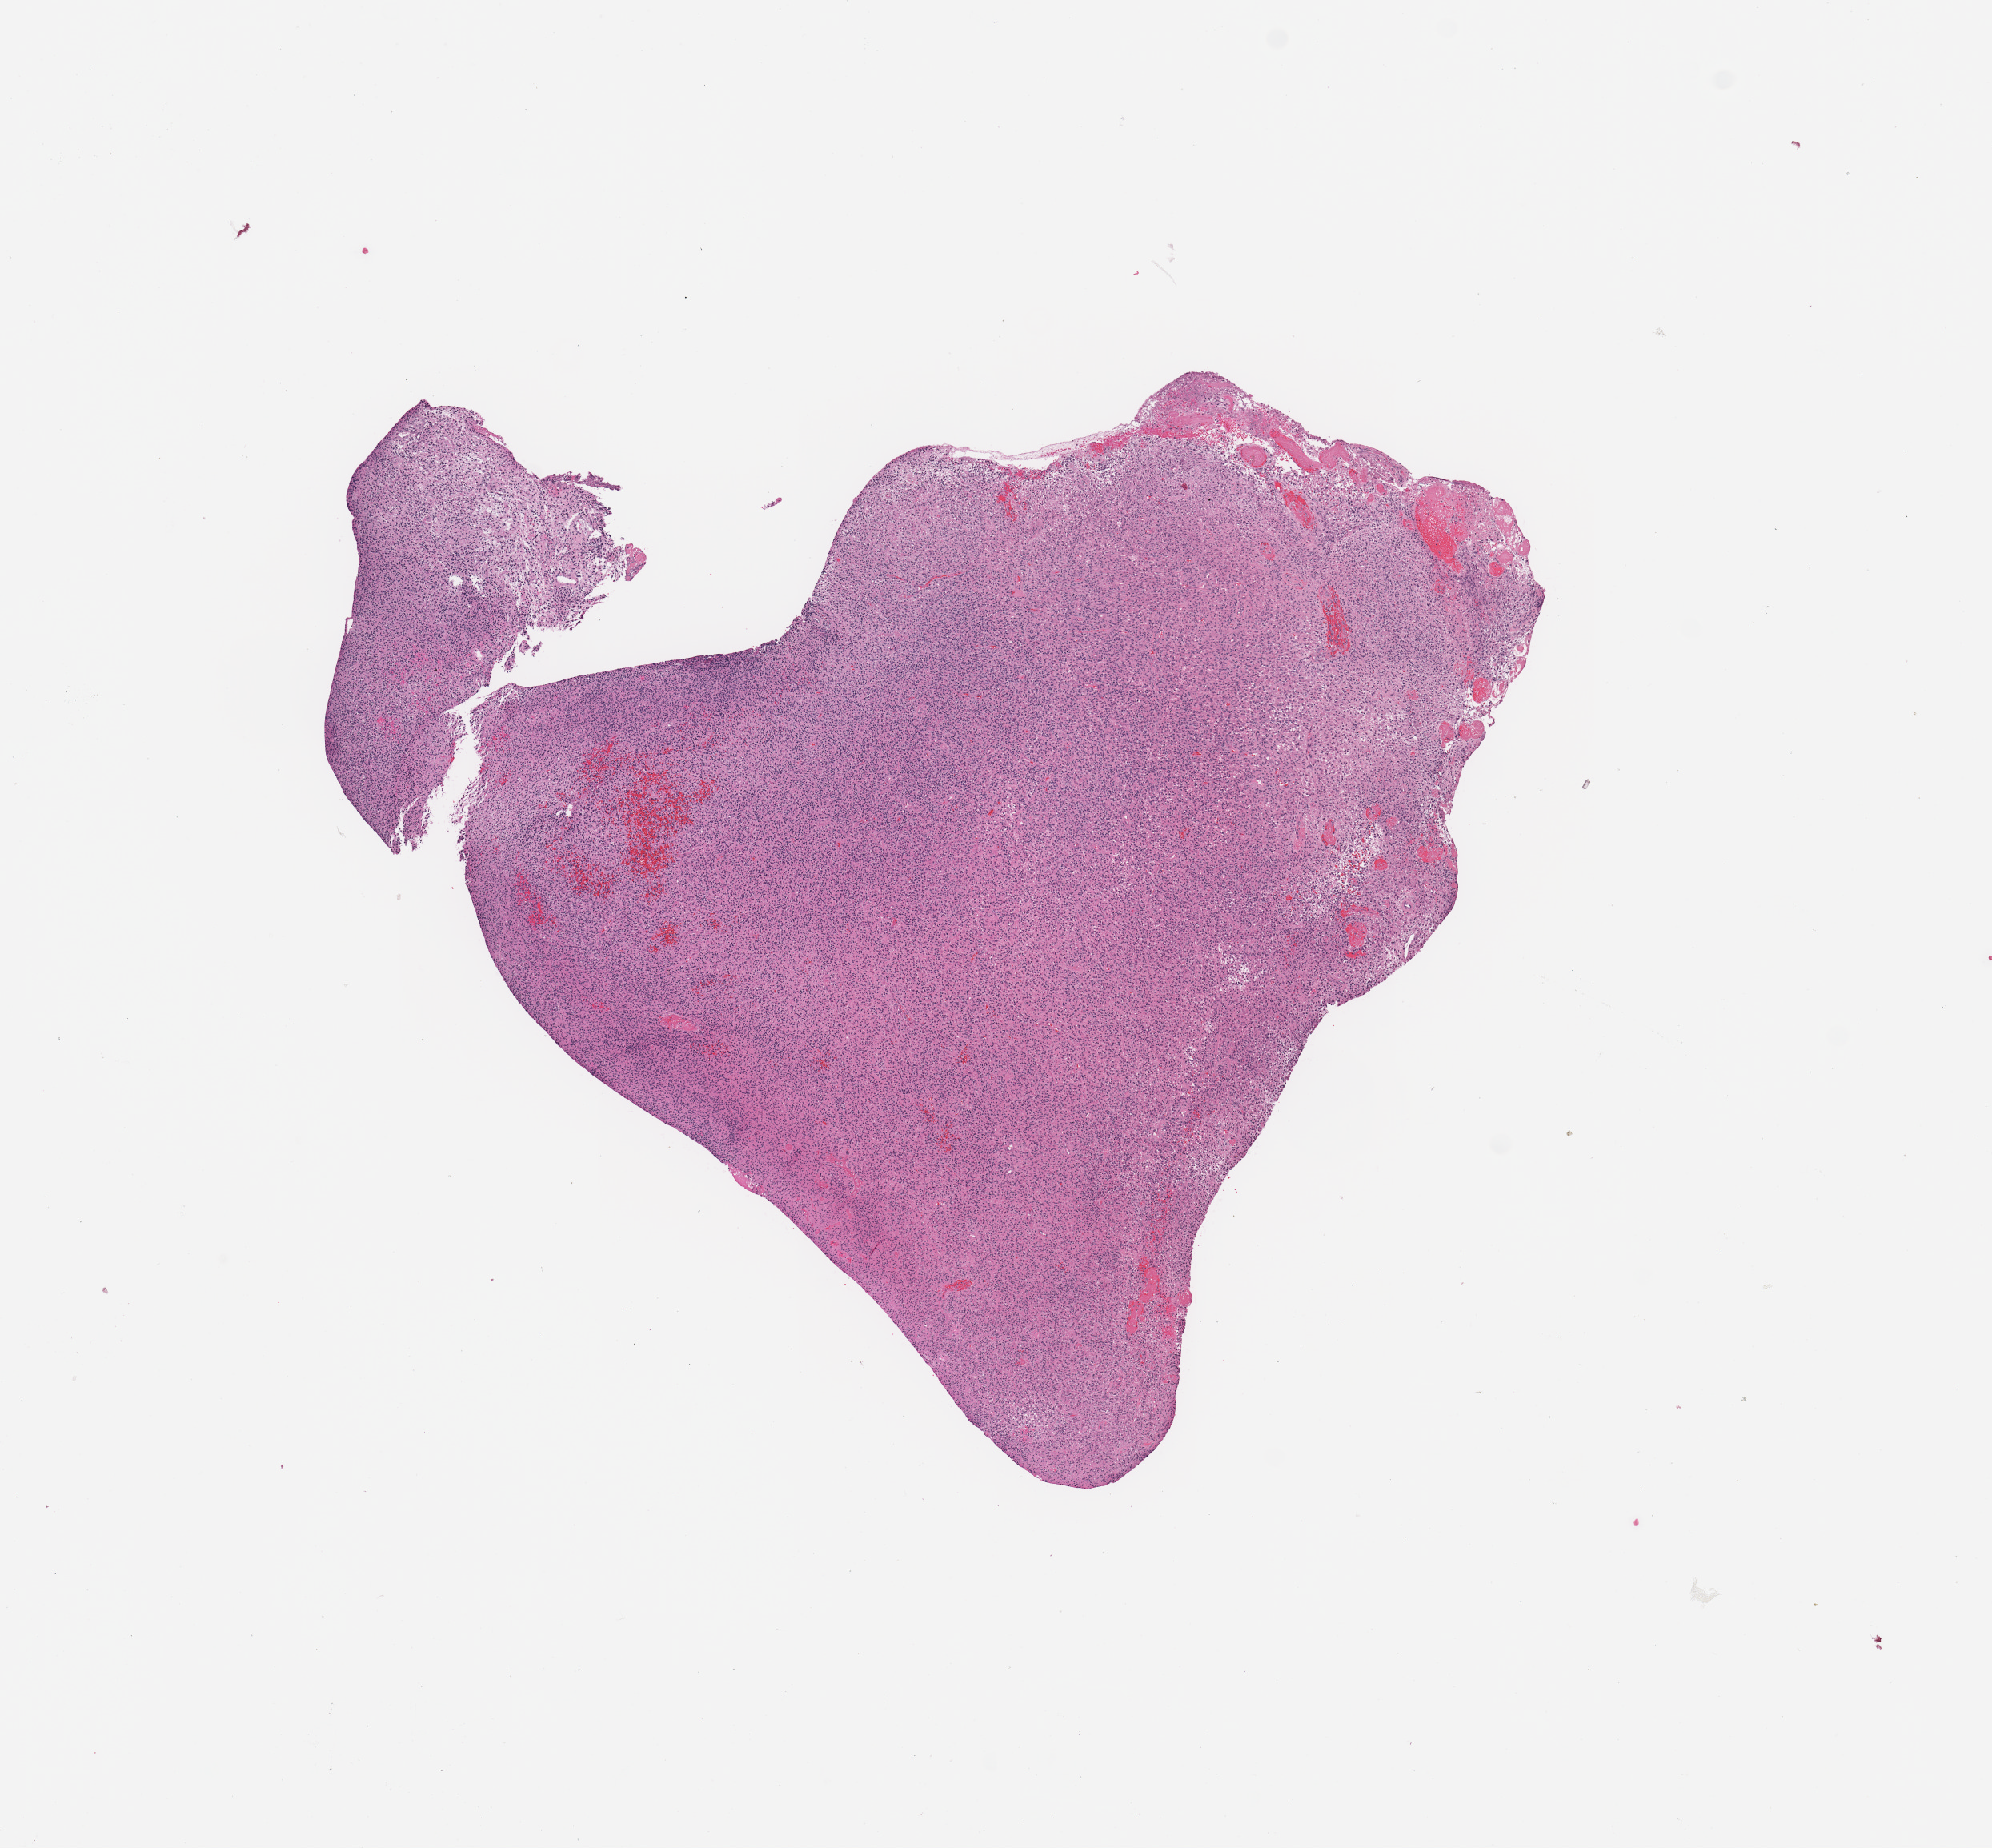
H&E whole-slide image — low-resolution overview of the scanned area, about 9.8 x 9.1 mm; tumour tissue sample, sampled site: brain. 51-year-old female patient. Pathologist review of this section (percent, as recorded): tumour nuclei 85%, necrosis 5%.
Diagnosis: Glioblastoma.